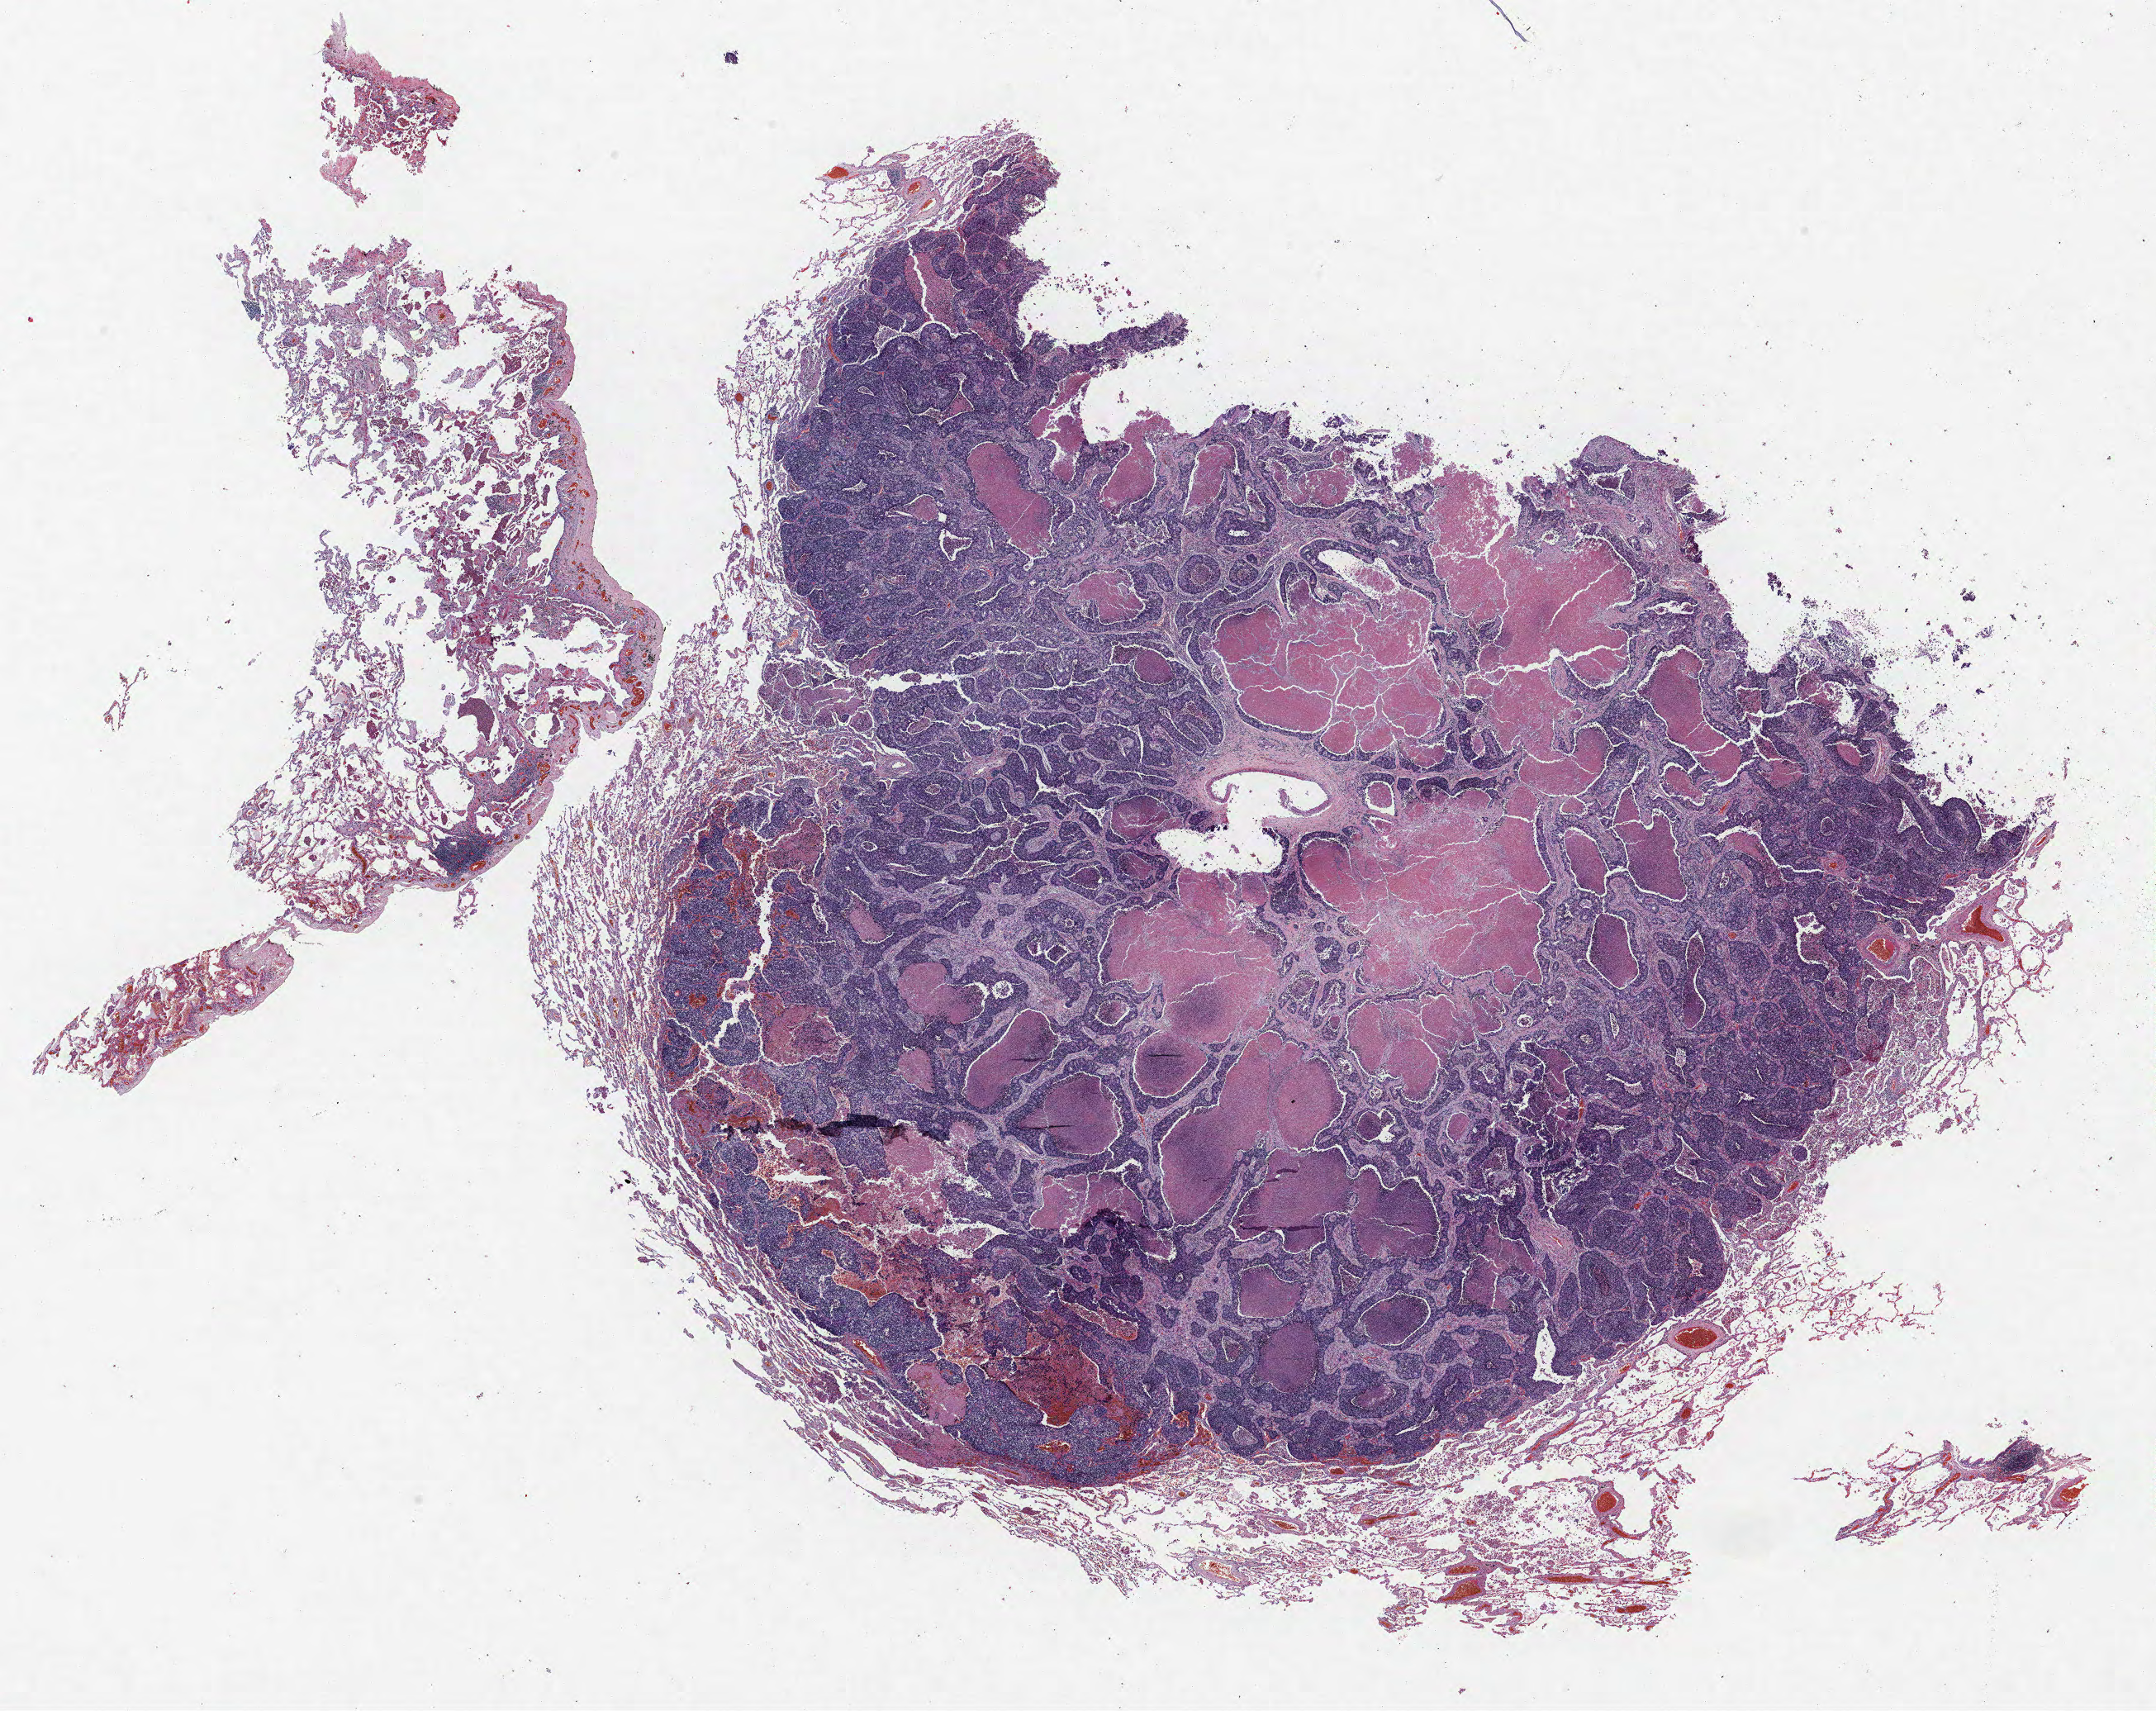
H&E whole-slide image — shown as a low-resolution overview of the whole scanned area (about 20.9 x 16.6 mm, slide scanned at 40x). Formalin-fixed paraffin-embedded (FFPE) section. Lung tissue. Male patient, aged 71 at enrolment. Current smoker at enrolment. Grade: poorly differentiated (G3).
Participant's lung-cancer diagnosis: Adenocarcinoma, NOS (ICD-O-3 8140/3). Stage (AJCC 6th edition): IIIB. Primary tumour location (clinical record): left upper lobe. Tumour size (pathology): 25 mm.